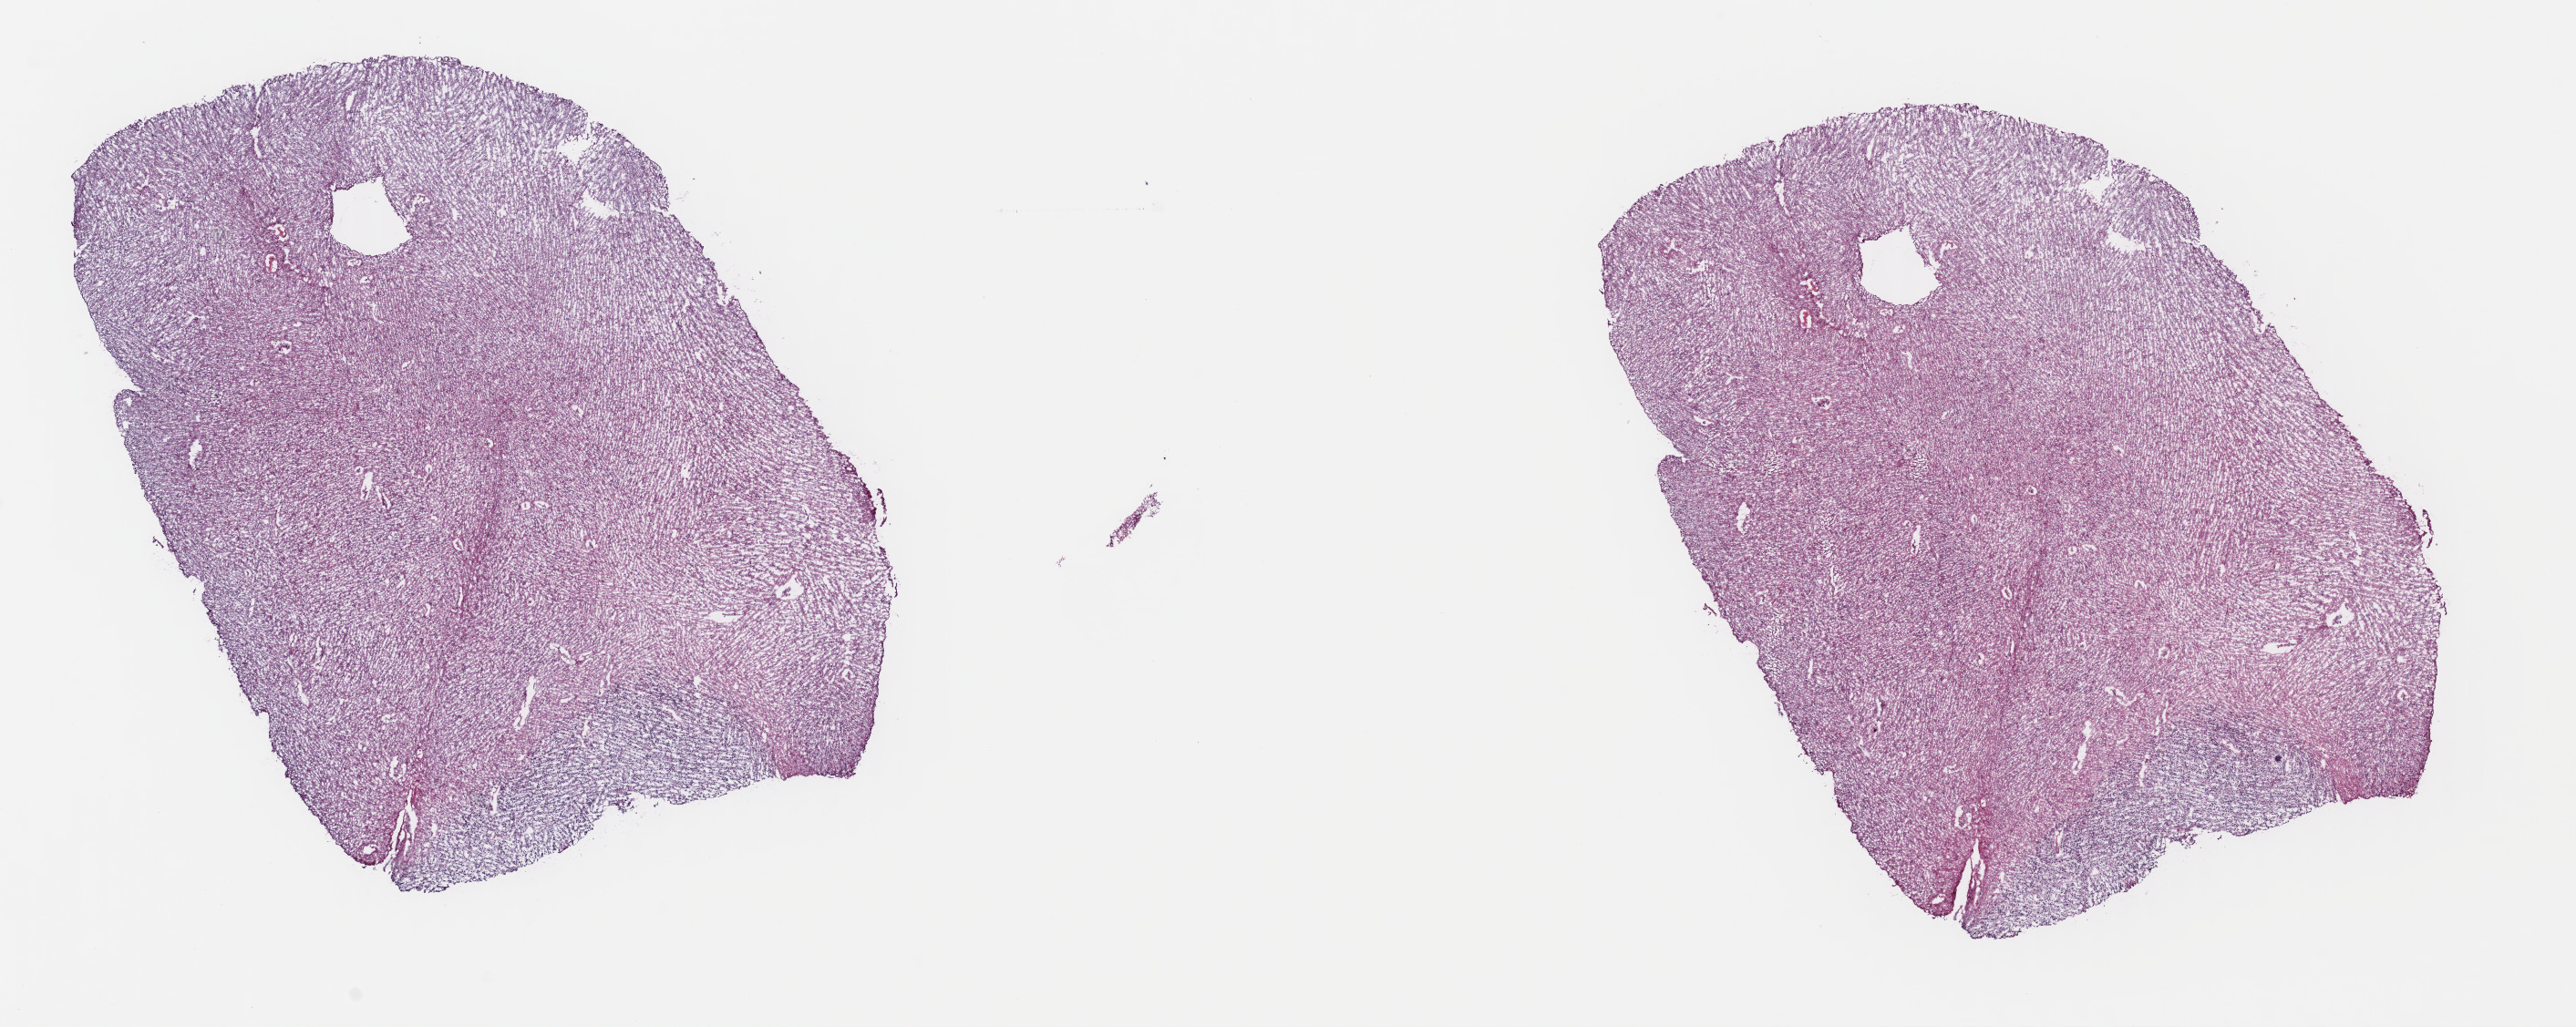
H&E whole-slide image — low-resolution overview of the scanned area, about 22.2 x 8.9 mm (acquisition: 40x scan); frozen section; brain, primary tumour sample. Male patient; age at initial diagnosis 49 years. Histologic grade: G2 (moderately differentiated). Pathologist review of this section (percent, as recorded): tumour cells 60%, tumour nuclei 90%, normal cells 10%, stromal cells 30%, necrosis 0%. Inflammatory infiltration, as recorded: lymphocyte infiltration 0%, monocyte infiltration 0%, neutrophil infiltration 0%.
* pathologic diagnosis: Oligodendroglioma, NOS (cerebrum)
* laterality: left